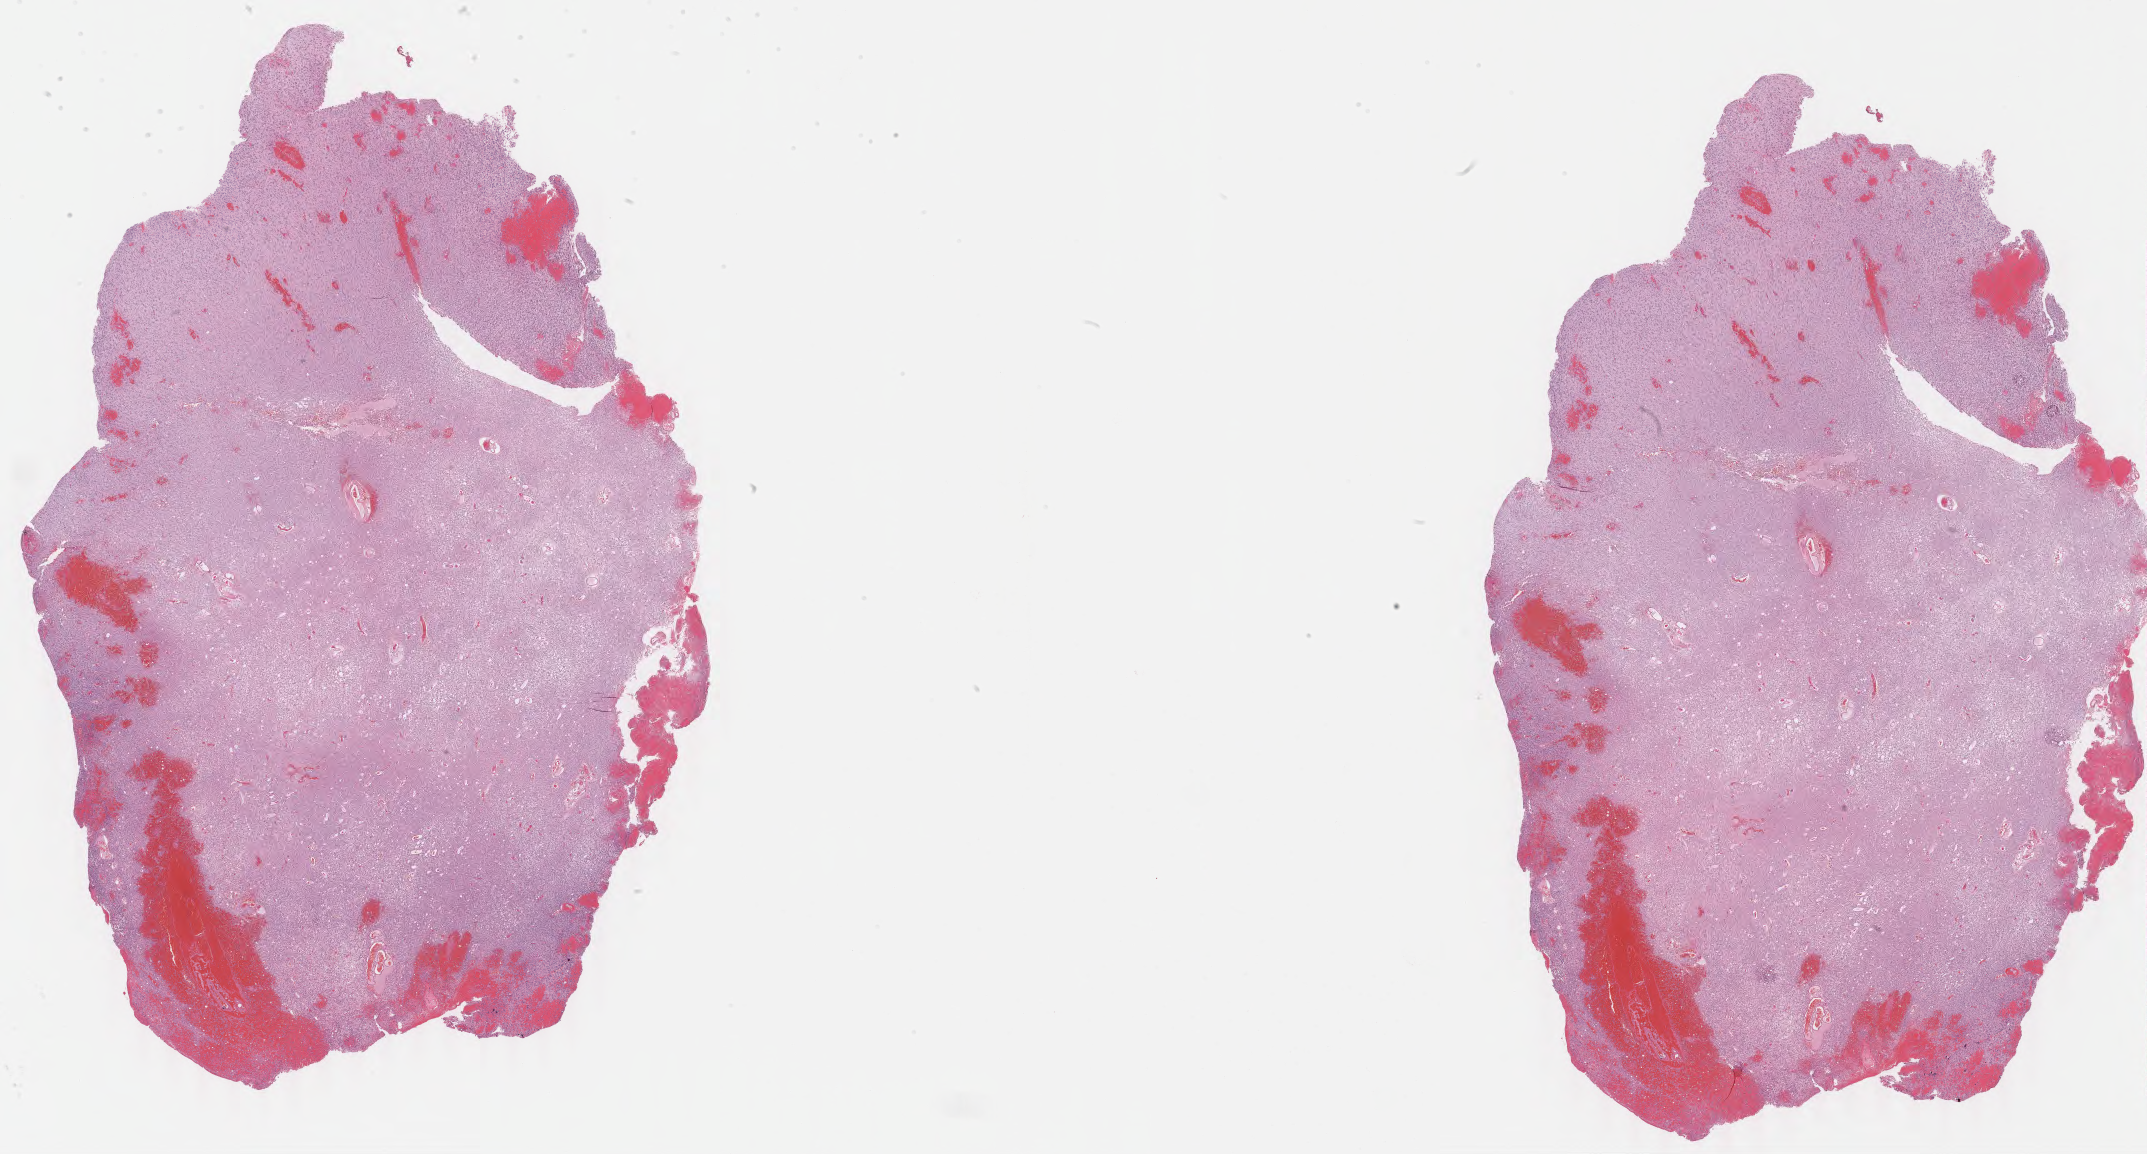
Whole-slide histology image, H&E — a low-resolution overview of the entire scanned area, about 33.9 x 18.2 mm; formalin-fixed paraffin-embedded (FFPE) diagnostic section; sample: primary tumour, brain. Female, age 55 years at initial diagnosis. Histologic grade: G3 (poorly differentiated).
* pathologic diagnosis: Mixed glioma